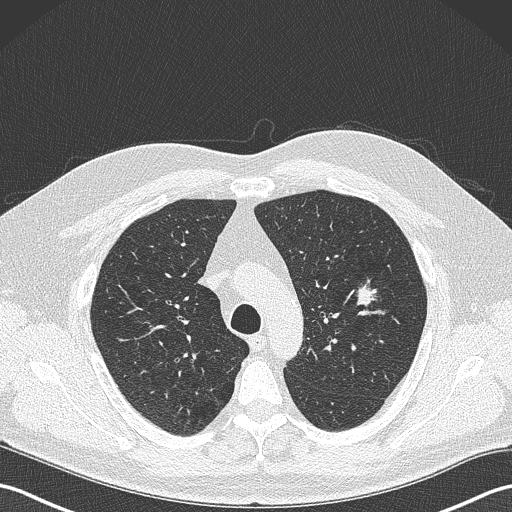
Axial slice from a low-dose chest CT screening exam; first (baseline) screen; lung window (W 1500 / L -600 HU); 1 mm slice thickness; lung (sharp) reconstruction kernel (B50f); slice 92 of 343 in the series; 512 × 512 image matrix. Male participant, aged 61 years at enrolment. Former smoker at enrolment.
- Lesion marked by an expert reader, bounding box [x1, y1, x2, y2] px = [348, 280, 385, 313].
- The screening reader recorded 2 non-calcified nodules or masses ≥4 mm on this exam (left upper lobe, lingula); which of them this box marks is not recorded.